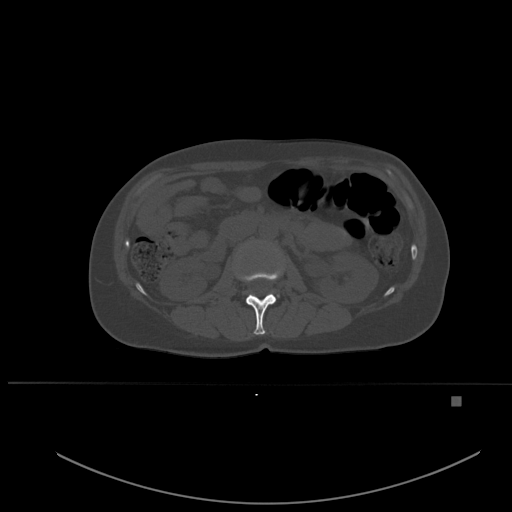
CT including the spine, one axial slice; position 226 of 651 along the scan axis; bone window (W 1800 / L 400 HU); 512 × 512 image matrix, field of view 443 × 443 mm. Patient: female, 49 years. From the clinical record (not read from this slice): primary cancer: breast; vertebrae with lytic lesions (as recorded): L3, T12, L4.
Structures marked on this image (semi-automatically segmented with operator editing):
- L1 vertebra: bounding box [x1, y1, x2, y2] px = [242, 271, 280, 335]
- L2 vertebra: [277, 295, 279, 297]